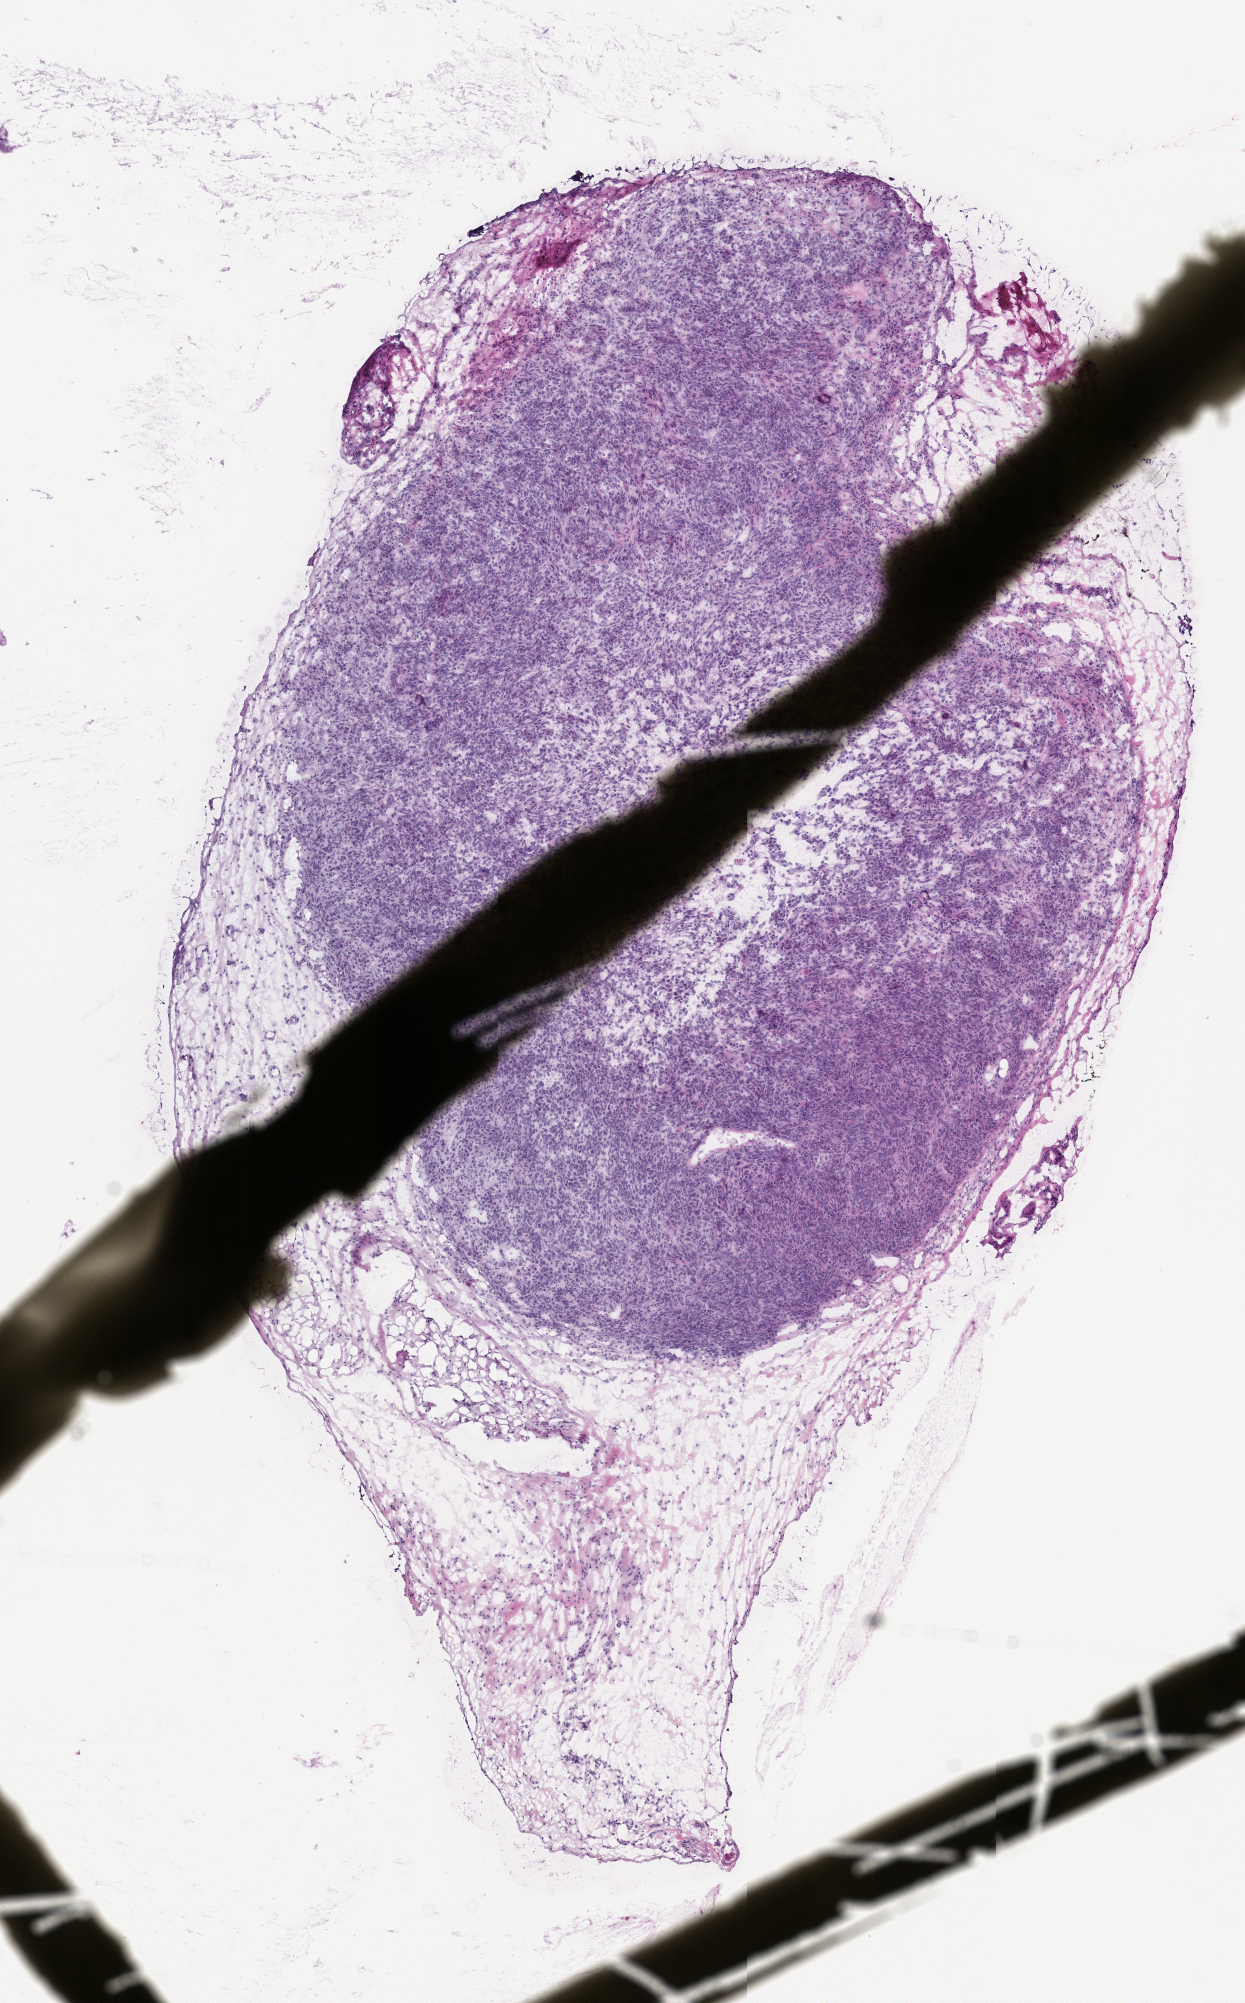
Whole-slide image, H&E: patient-derived xenograft (human tumor grown in a mouse), passage 2 — a low-resolution overview of the entire scanned area, about 5.0 x 8.1 mm, formalin-fixed, paraffin-embedded (FFPE) tissue, tumor site category: musculoskeletal.
Originating patient diagnosis: Spindle Cell Sarcoma.